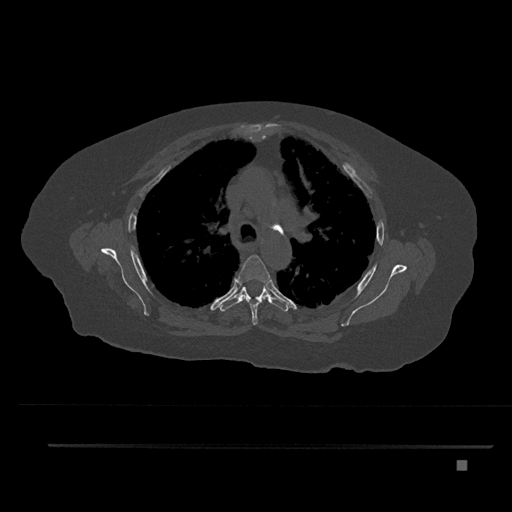
CT including the spine, one axial slice. Position 585 of 797 along the scan axis. Reconstruction kernel Br40s/3. 120 kVp. Bone window (W 1800 / L 400 HU). 512 × 512 image matrix, field of view 437 × 437 mm. Patient: female, 76 years. From the clinical record (not read from this slice): primary cancer: lung; vertebrae with lytic lesions (as recorded): T11, L3.
Annotated regions visible in this slice (semi-automatically segmented with operator editing):
- T4 vertebra: bounding box (x1, y1, x2, y2) in pixels: (237, 255, 271, 325)
- T5 vertebra: (220, 281, 288, 312)